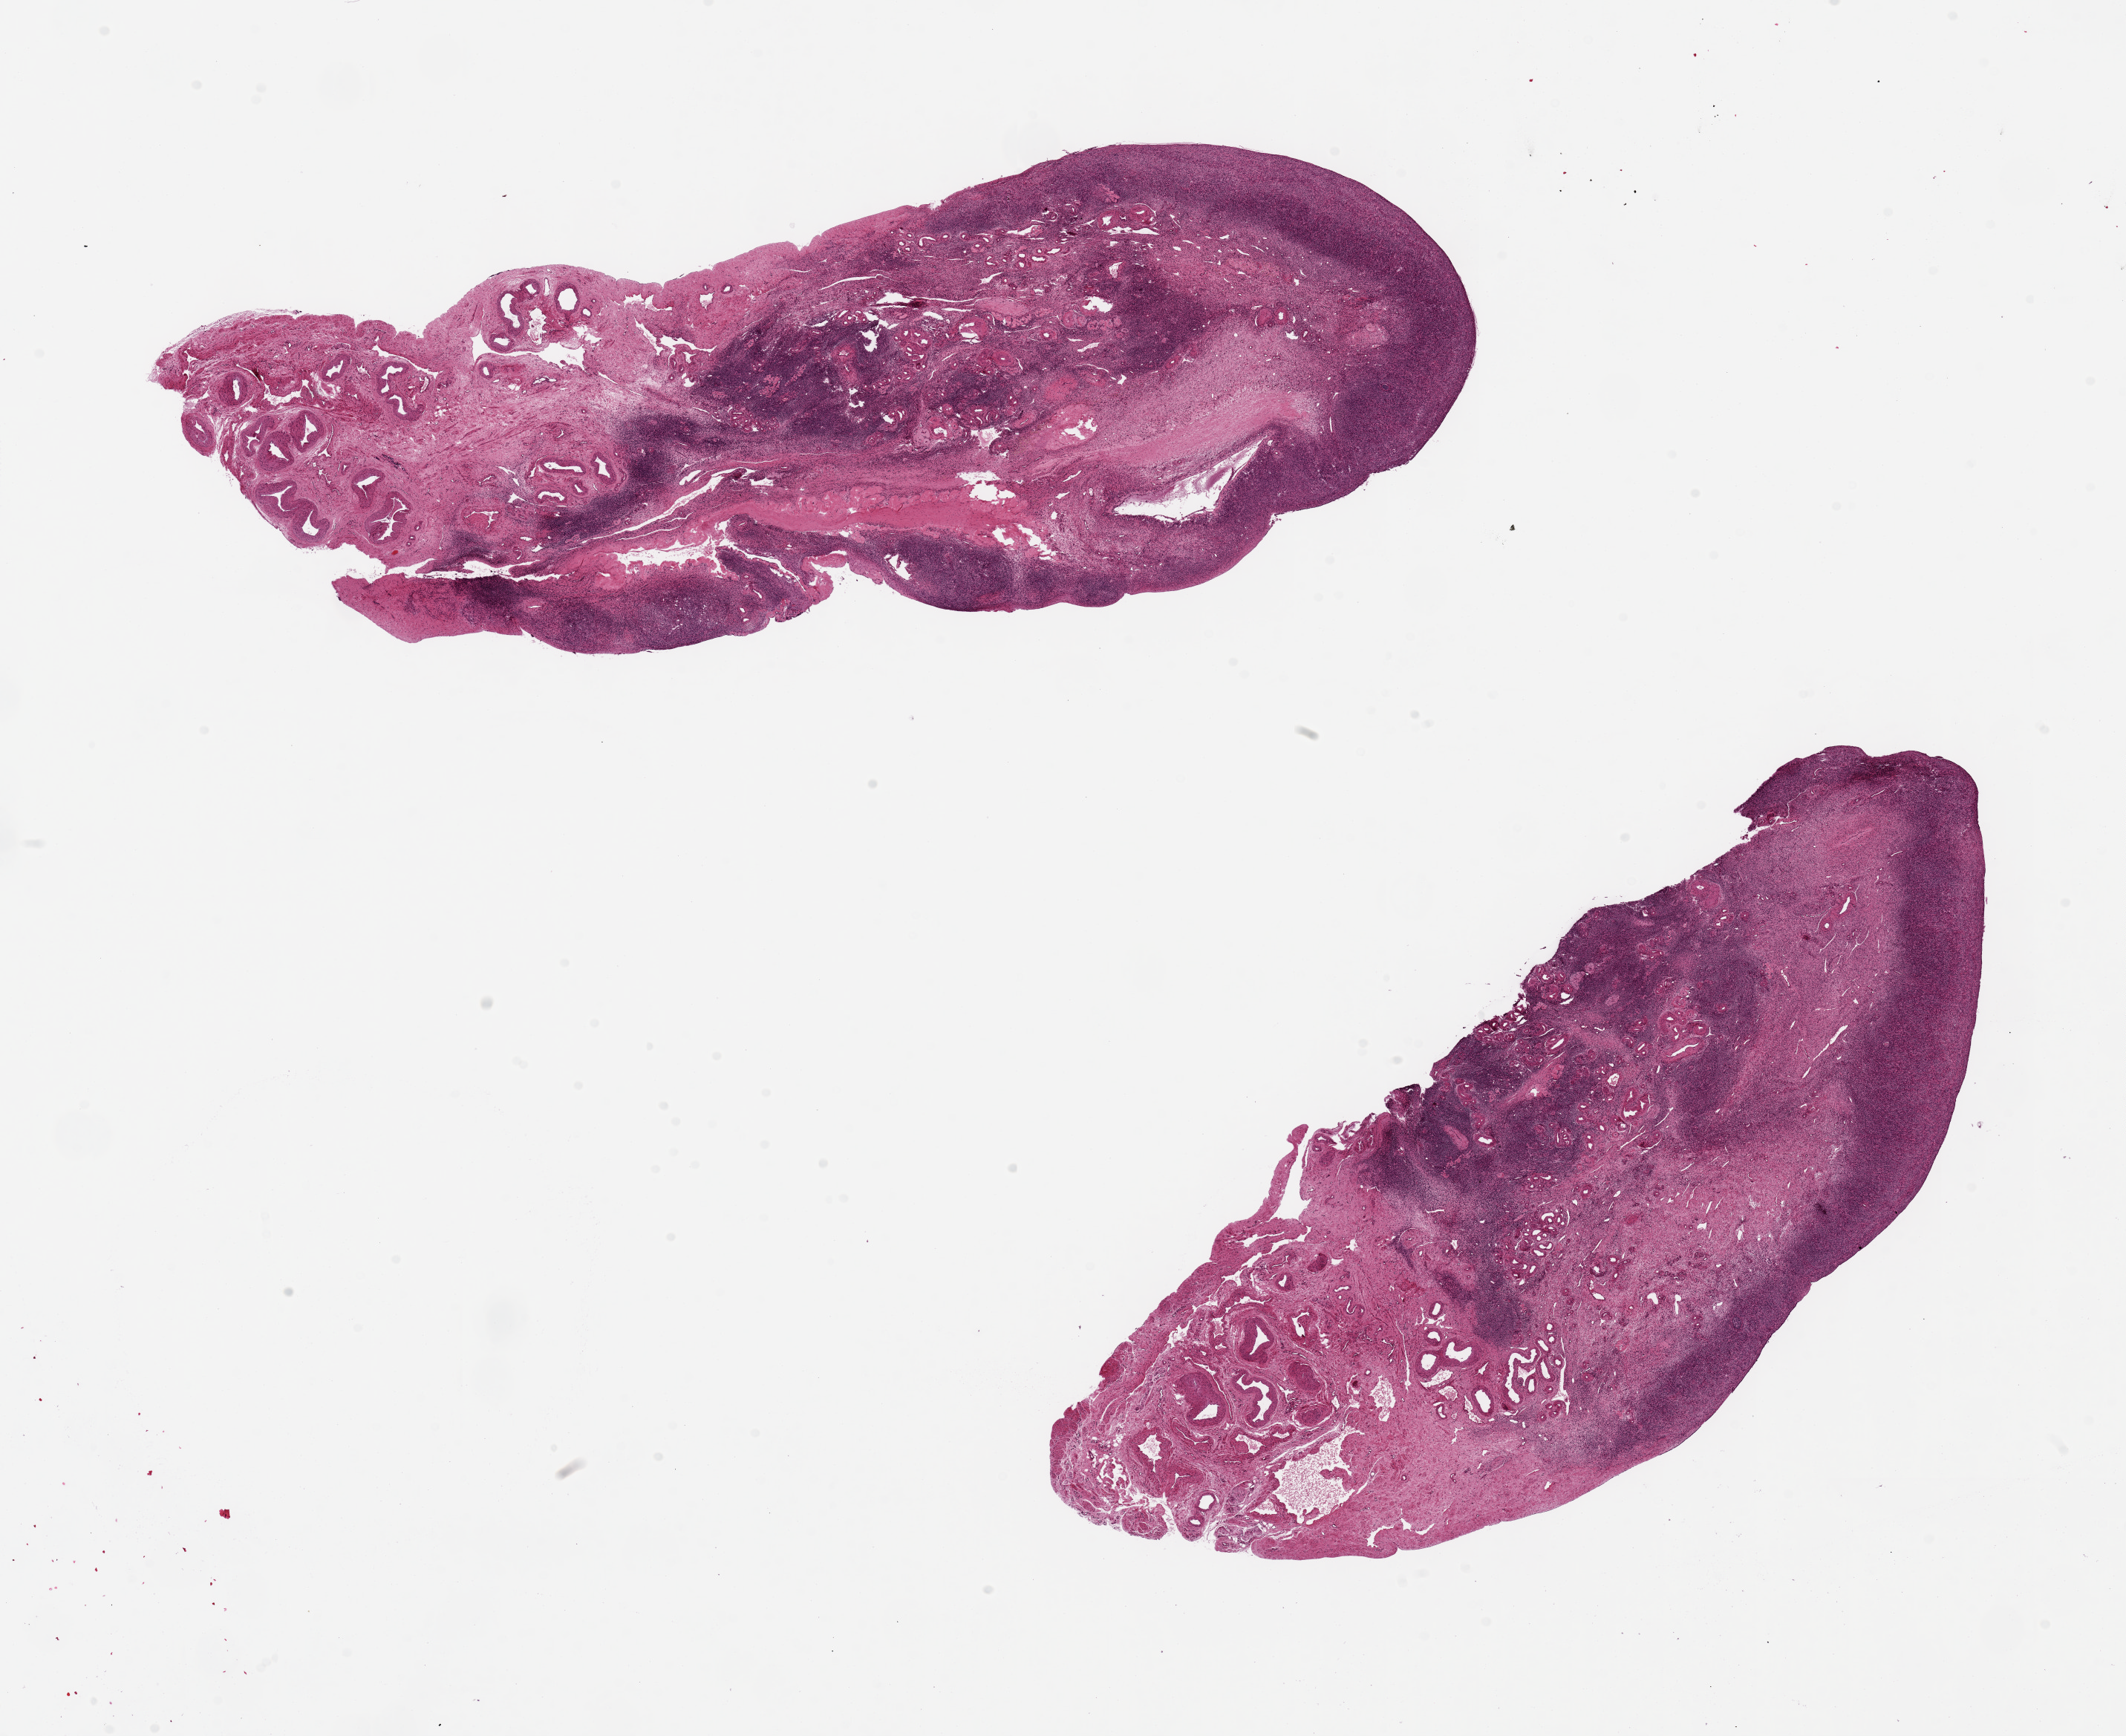
Whole-slide image, haematoxylin and eosin stain — a low-resolution overview of the entire scanned area, about 22.6 x 18.5 mm. PAXgene-fixed, paraffin-embedded tissue. Section of ovary (target tissue). Tissue donor sample. Donor: female.
• pathologist's review note for this sample: 2 pieces ~12x5 , post menopausal appearance, minute (~0.1mm) transitional cell islets noted, ? incipient Brenner tumors